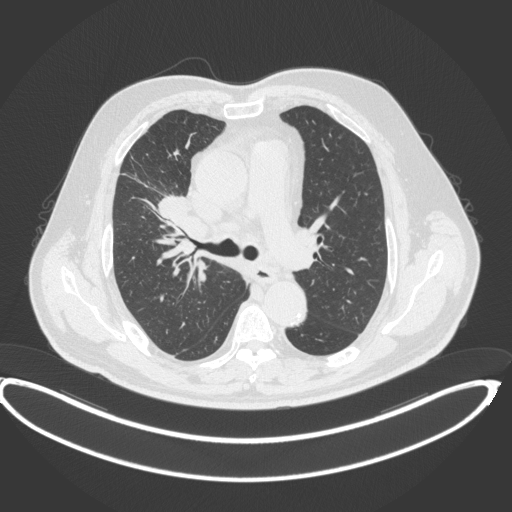
Chest CT, one axial slice. Slice 263 of 395 in the series (ordered by position). Reconstruction kernel B31f. Lung window (W 1500 / L -600 HU). 512 × 512 image matrix. Patient: male, 62 years. Case-level facts recorded for this patient, not image findings: clinical TNM (as recorded): T1c N3 M1c.
Outlined on this slice (rectangle marked by the reading radiologist):
- lung tumour (recorded histology: adenocarcinoma): bounding box [x1, y1, x2, y2] px = [153, 189, 192, 221]